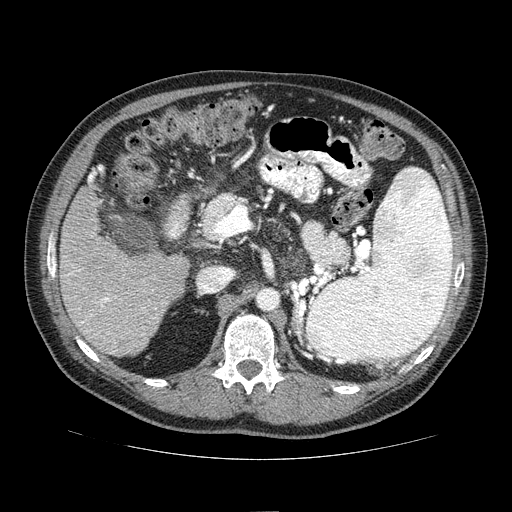
Contrast-enhanced abdominal CT (liver protocol), one axial slice; slice 31 of 81 in the series (ordered by position); one of 2 acquisitions stored at this slice position; soft-tissue window (W 400 / L 40 HU); 2.5 mm slice thickness; 512 × 512 image matrix, field of view 400 × 400 mm. From the clinical record (not read from this slice): diagnosis: hepatocellular carcinoma (patient treated with transarterial chemoembolisation; whether this scan precedes or follows treatment is not stated here); TNM stage (as recorded): Stage-IIIA; Child-Pugh class: A; tumour differentiation: well differentiated; tumour nodularity: multinodular.
Annotated regions visible in this slice (semi-automatic segmentation, software-assisted and operator-edited):
- liver parenchyma outside the tumour (the mass and vessels are separate outlines, so this box may not span the whole liver): bounding box (x1, y1, x2, y2) in pixels: (60, 174, 190, 356)
- liver vessels: (67, 175, 144, 353)